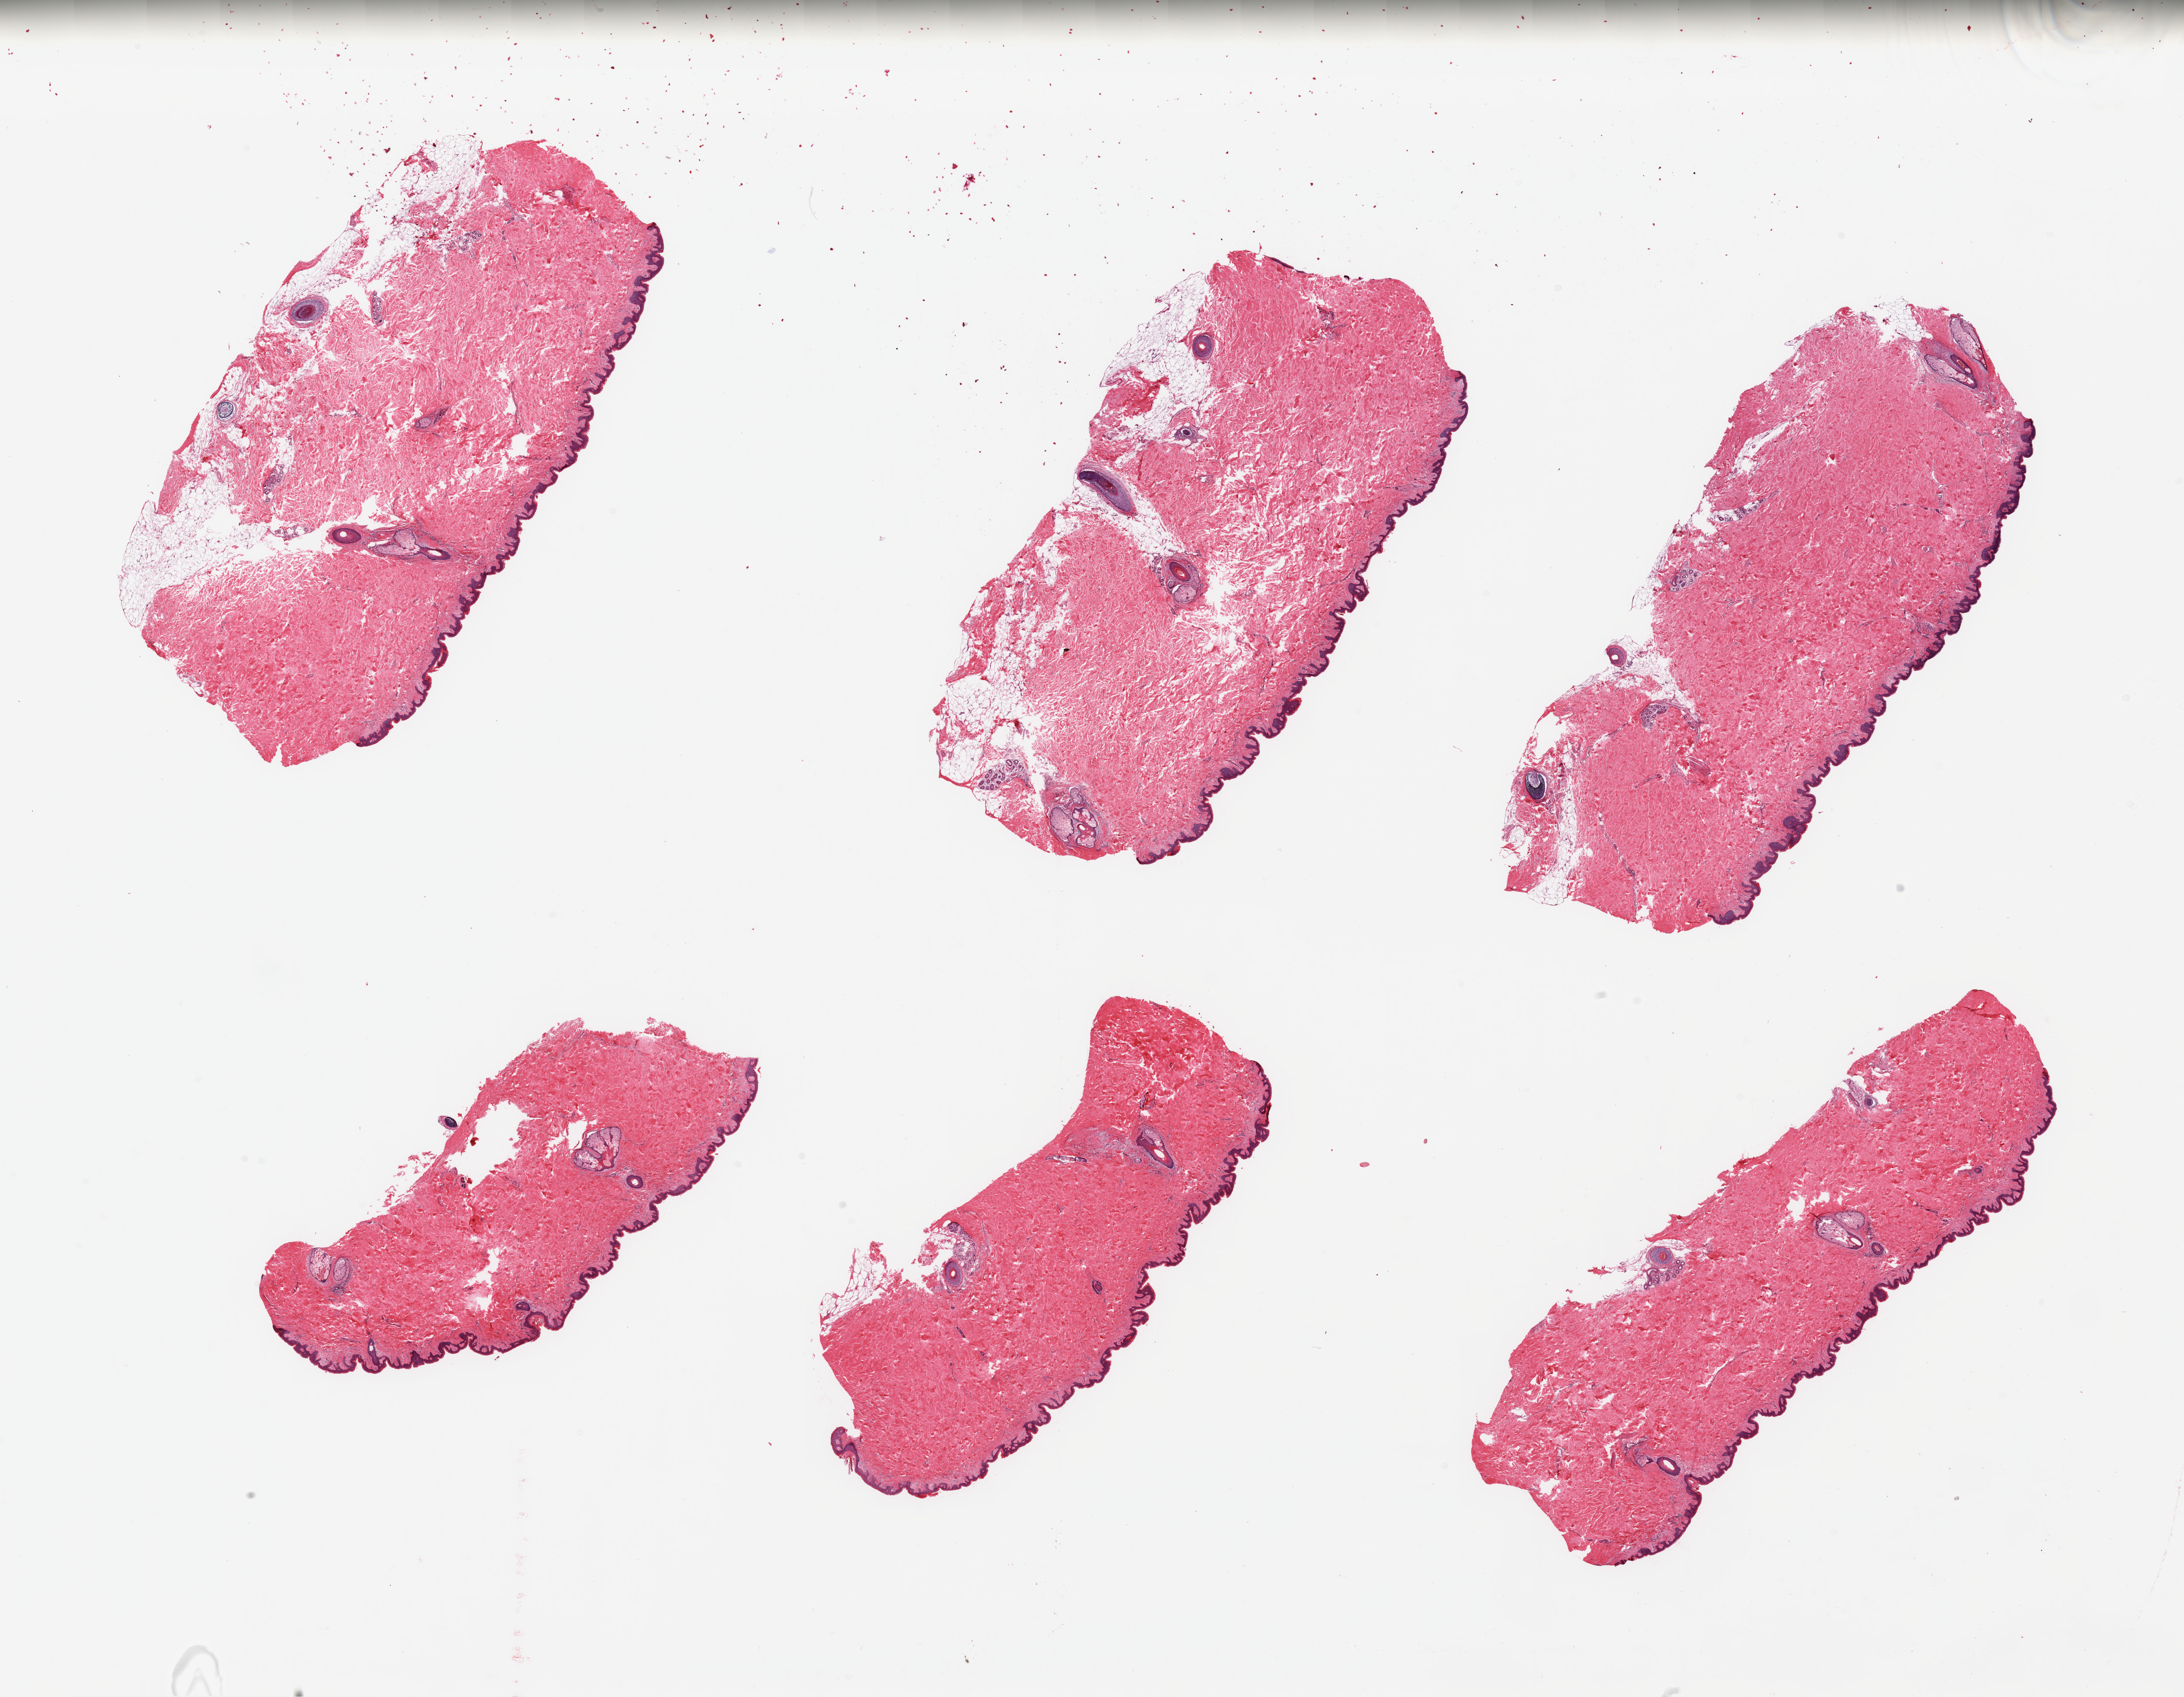
Digitized hematoxylin and eosin (H&E)-stained section, brightfield — a low-resolution overview of the entire scanned area, about 29.5 x 23.0 mm (acquisition: 20x scan), PAXgene-fixed, paraffin-embedded tissue, target tissue: skin of suprapubic region, tissue donor sample. Male donor.
• reviewer comment on this tissue sample: 6 pieces; mostly well trimmed, but few include ~10% fat